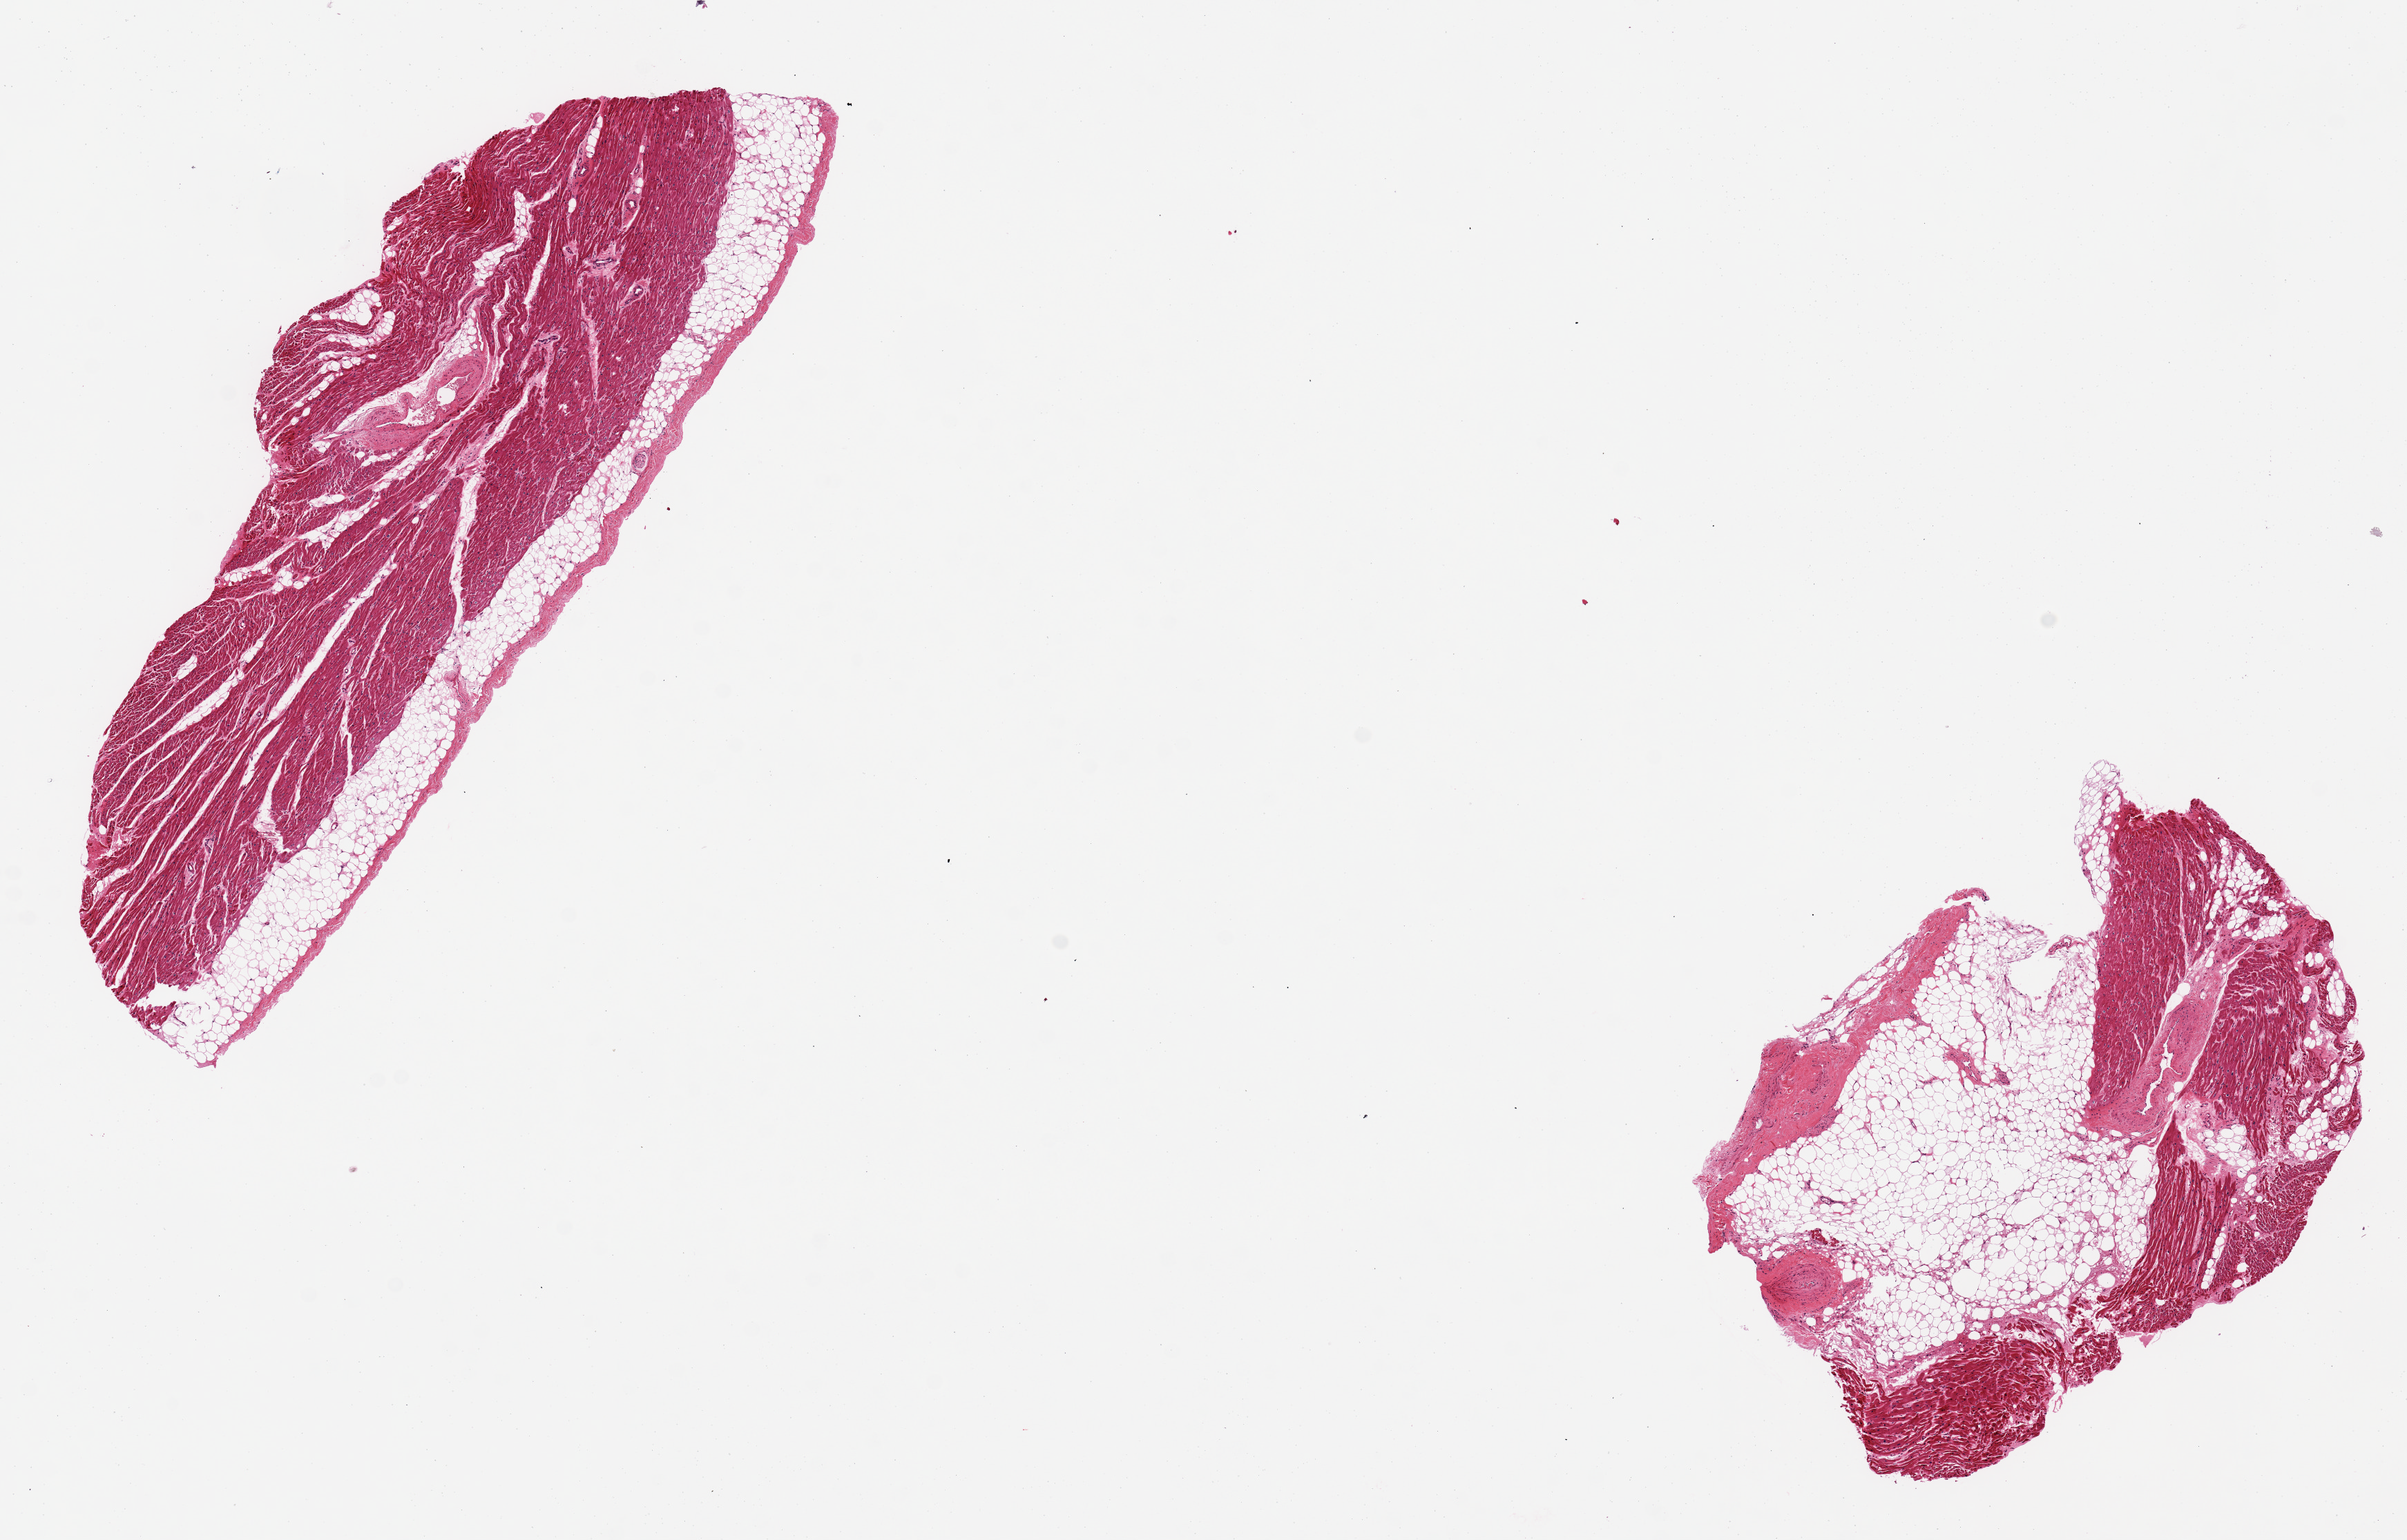
Digitized H&E-stained section, brightfield, a low-resolution overview of the entire scanned area, about 13.8 x 8.8 mm (from a 20x scan). PAXgene-fixed paraffin-embedded (PFPE) section. Sampled site (target tissue): coronary artery. Tissue donor sample.
Reviewer comment on this tissue sample: No artery present: myocardium + fat. Minute (0.5mm intramuscular vessel noted.